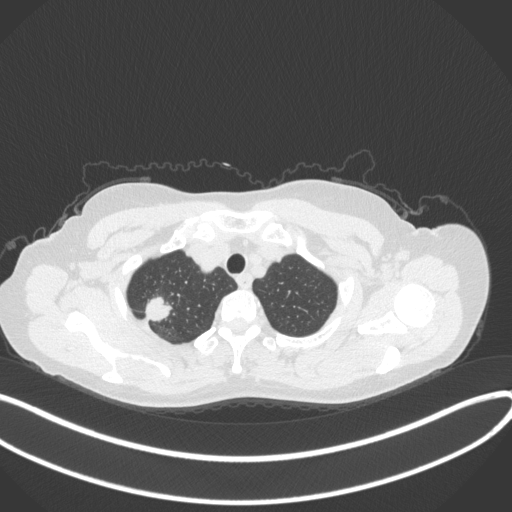
Chest CT, one axial slice; position 319 of 342 along the scan axis; 120 kVp; lung window (W 1500 / L -600 HU); 512 × 512 image matrix. Patient: female, 50 years. From the clinical record (not read from this slice): clinical TNM (as recorded): T1c N0 M0; histopathological grade: G2-3.
Outlined on this slice (rectangle marked by the reading radiologist):
- lung tumour (recorded histology: adenocarcinoma): bounding box [x1, y1, x2, y2] px = [140, 290, 175, 327]